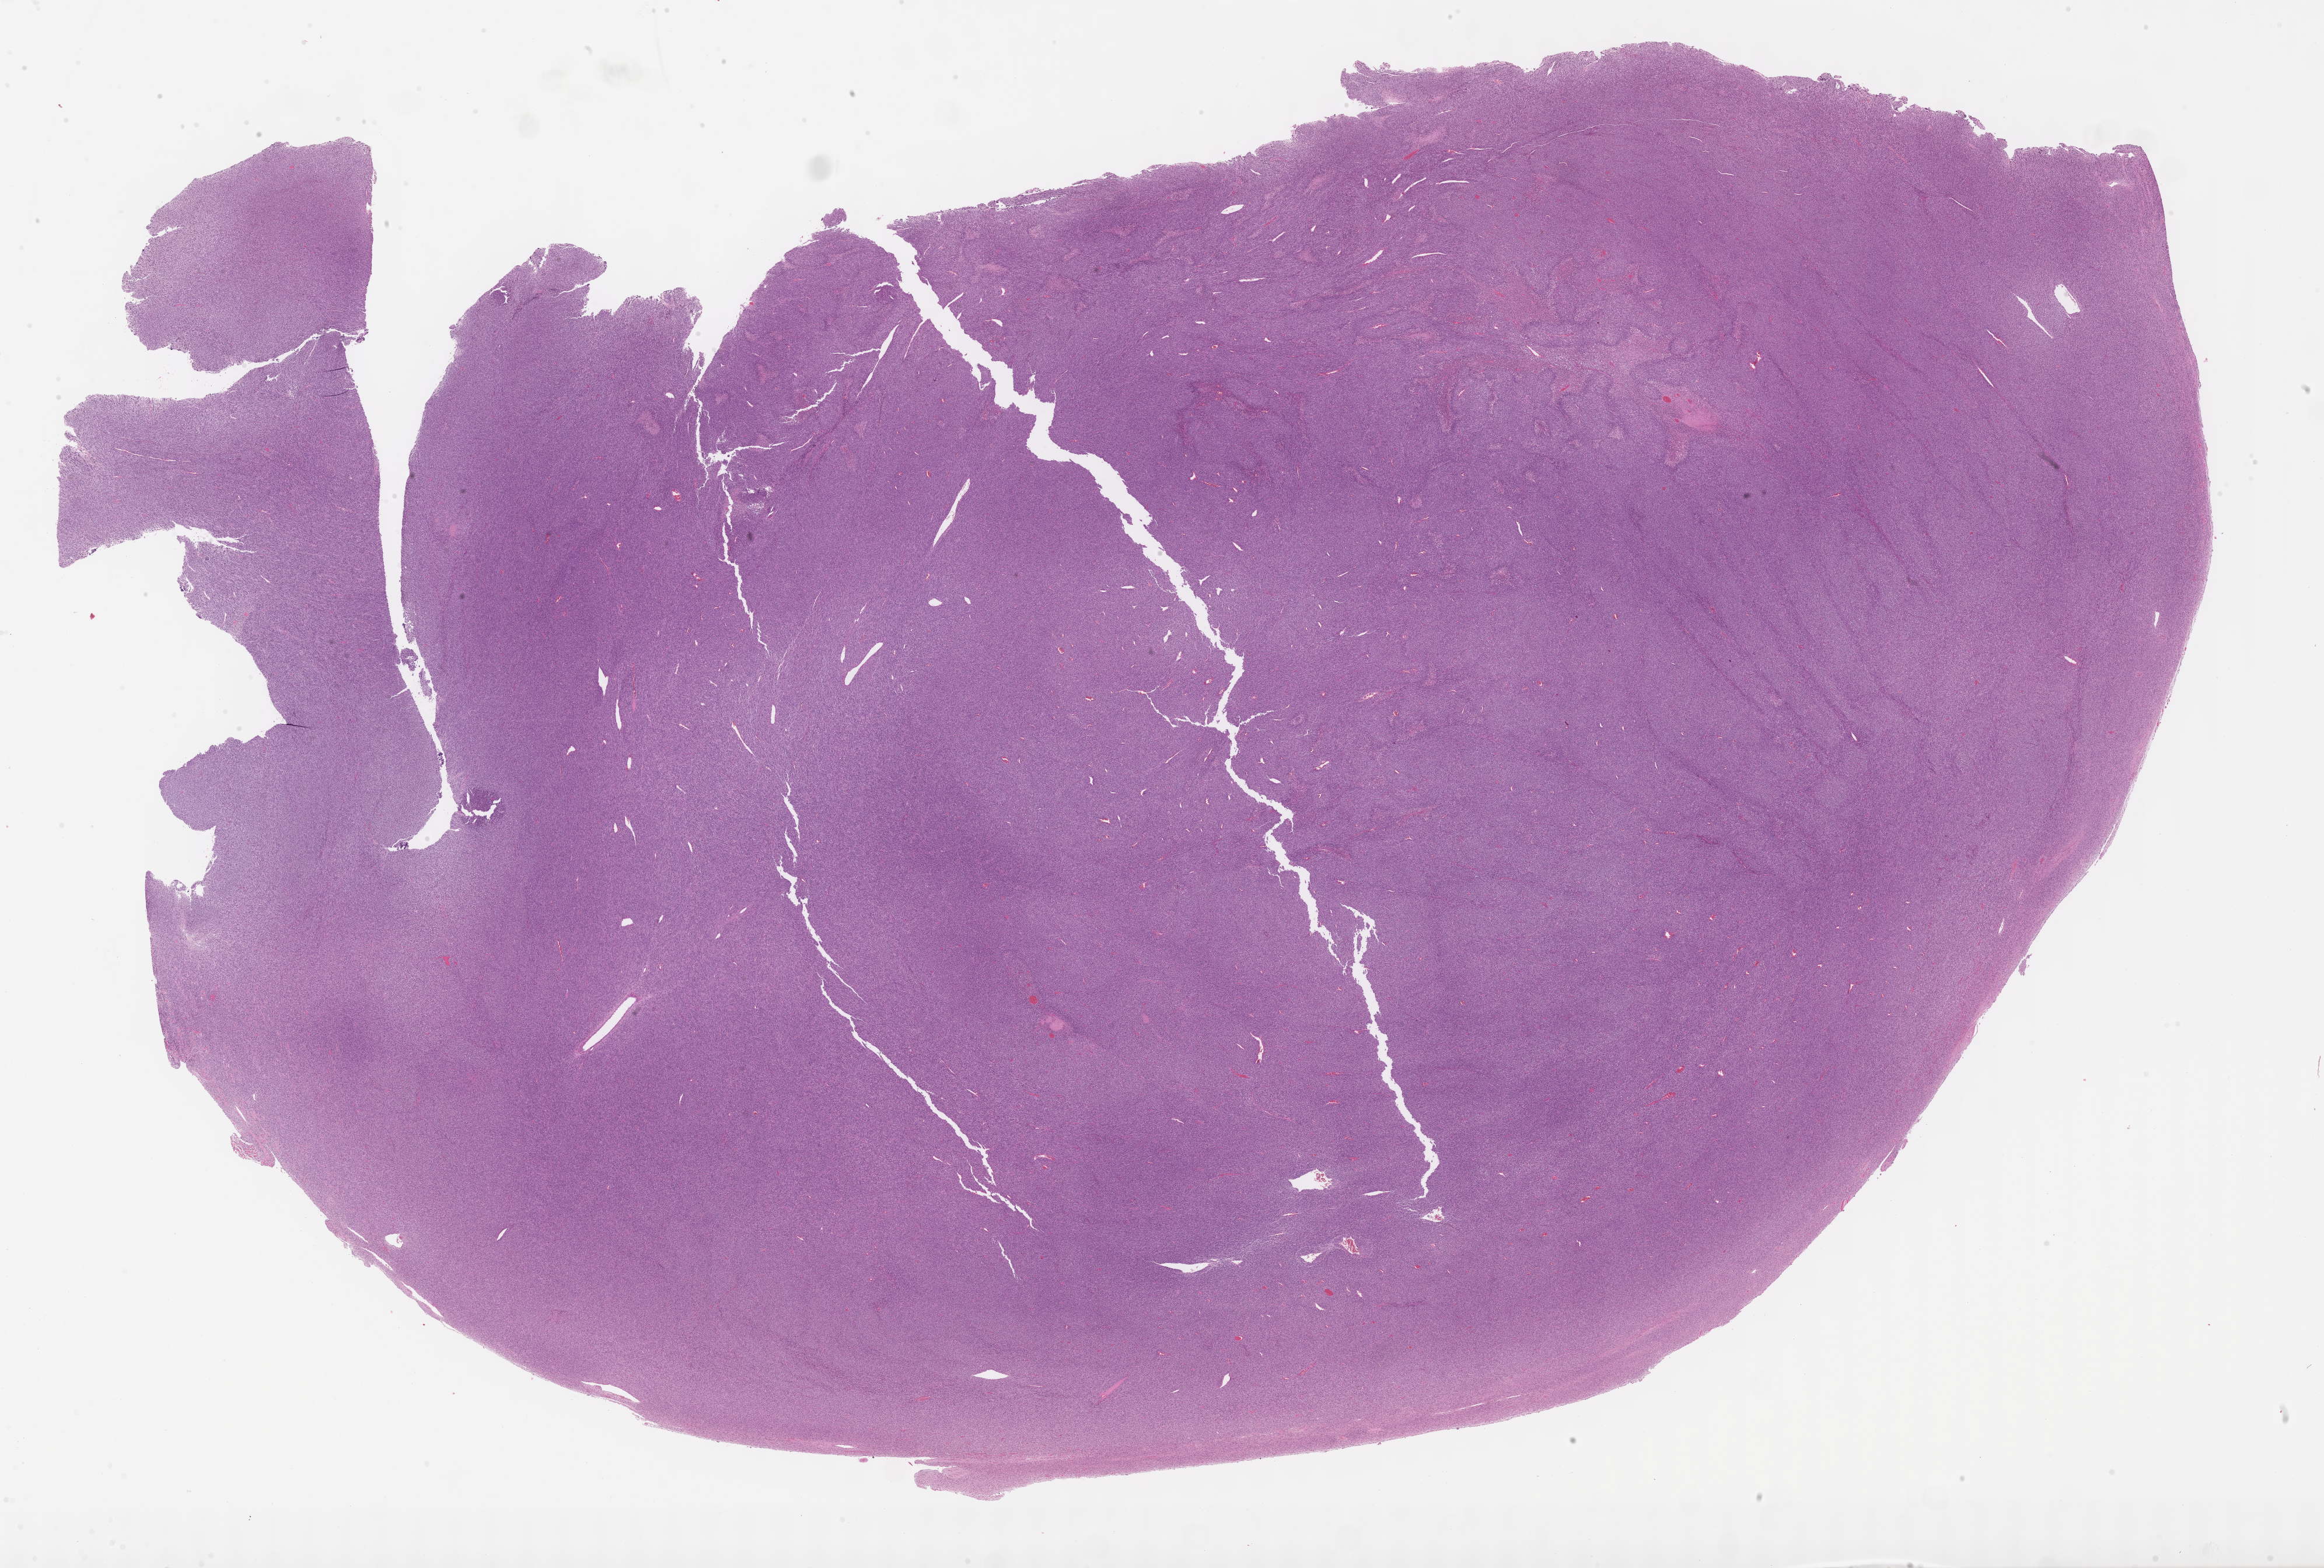
H&E whole-slide image of tumor tissue, whole scanned area (about 32.2 x 21.7 mm) shown as a low-resolution overview; formalin-fixed, paraffin-embedded (FFPE) tissue; site: soft tissue, back-left. Male patient, age at diagnosis 0.1 years.
Diagnosis: rhabdomyosarcoma; histological classification: spindle cell rhabdomyosarcoma.